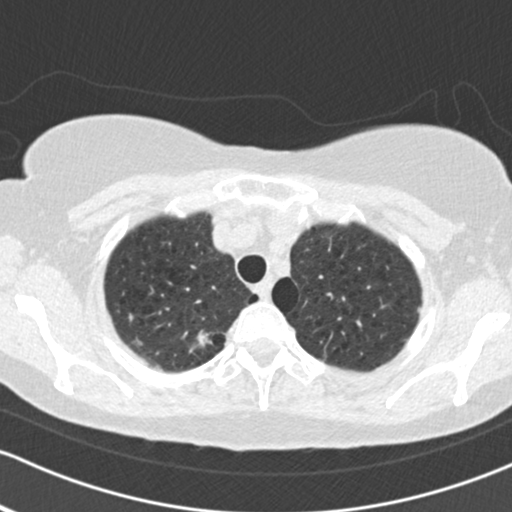
Axial slice from a low-dose chest CT screening exam. Second screening round (one year after baseline). Lung window (W 1500 / L -600 HU). 2 mm slice thickness. Standard (soft-tissue) reconstruction kernel (B30f). 120 kVp. Female participant, aged 64 years at enrolment.
Expert reader's lesion annotation, bounding box (x1, y1, x2, y2) in pixels: (172, 320, 228, 373). Screening reader's record for this exam (one nodule recorded; not confirmed to be the boxed lesion): non-calcified nodule or mass ≥4 mm, right upper lobe, 16 × 15 mm, spiculated (stellate) margins, soft tissue attenuation, pre-existing on the prior screen: no. Official screen result: positive, other.